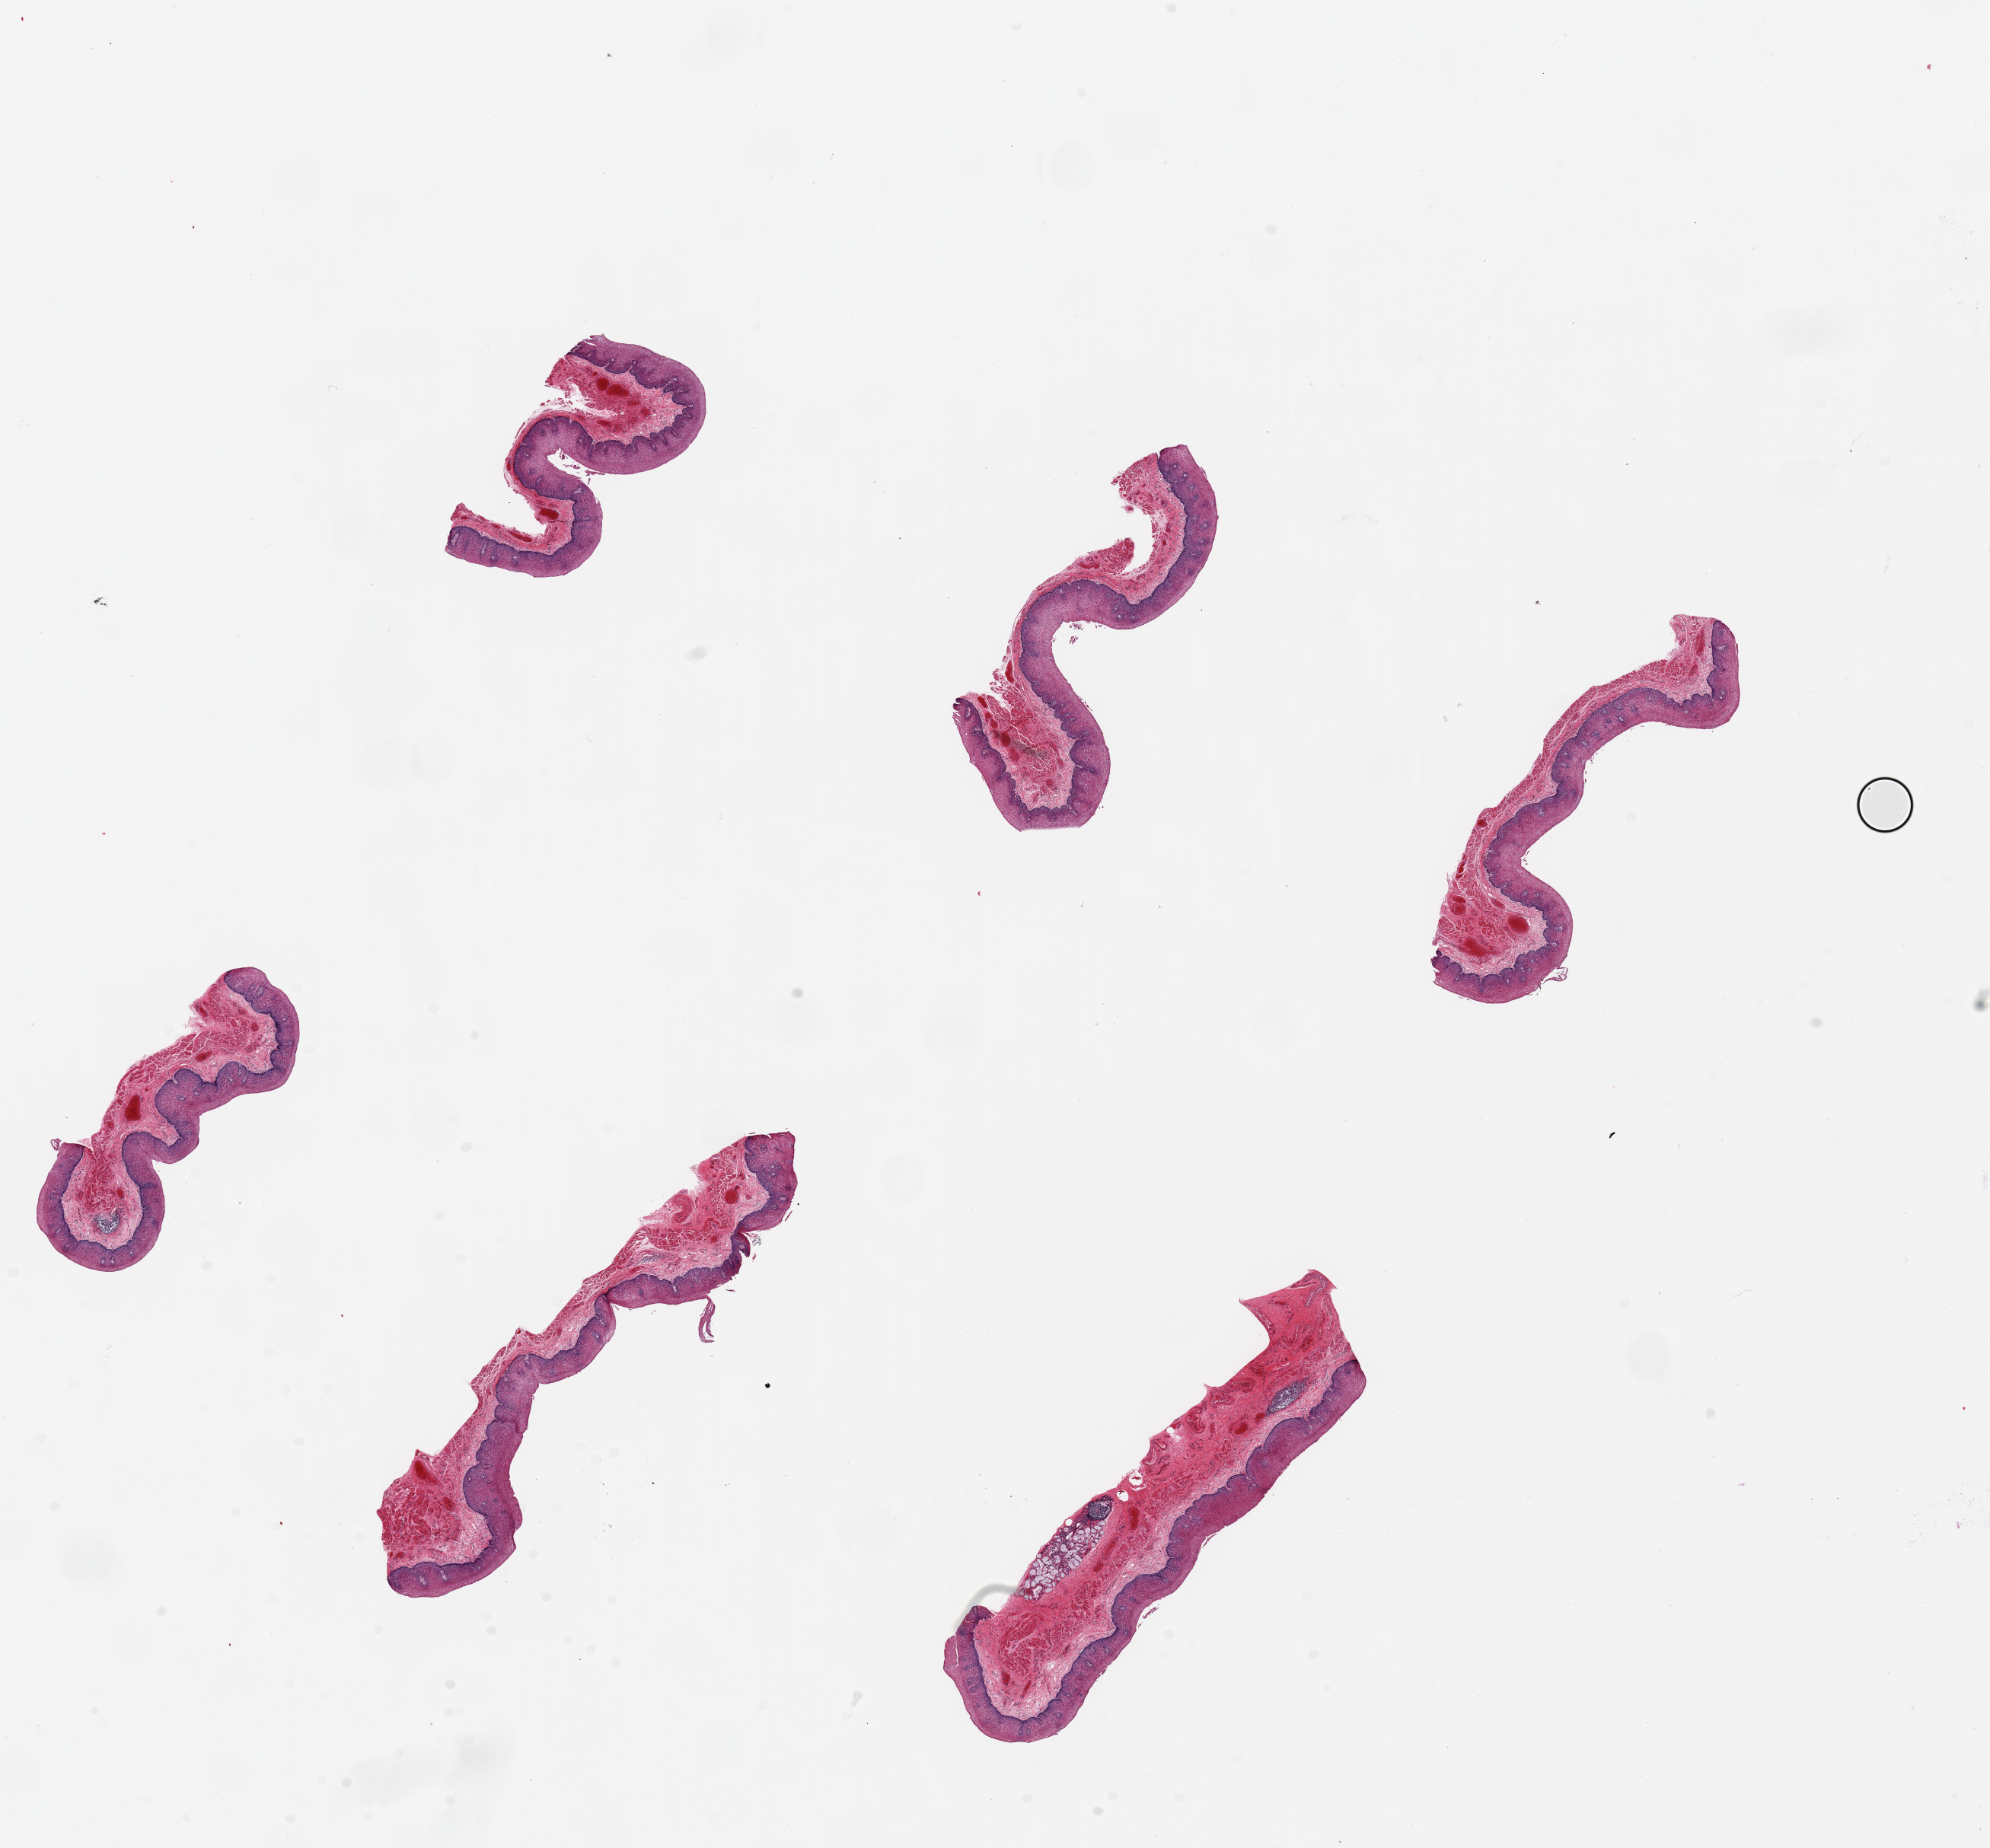
H&E whole-slide image — whole scanned area (about 20.7 x 19.2 mm) shown as a low-resolution overview; PAXgene-fixed paraffin-embedded (PFPE) section; target tissue: esophageal mucous membrane; tissue donor sample.
* review note (as recorded): 6 pieces ~8x3mm, up to 50% squamous mucosa